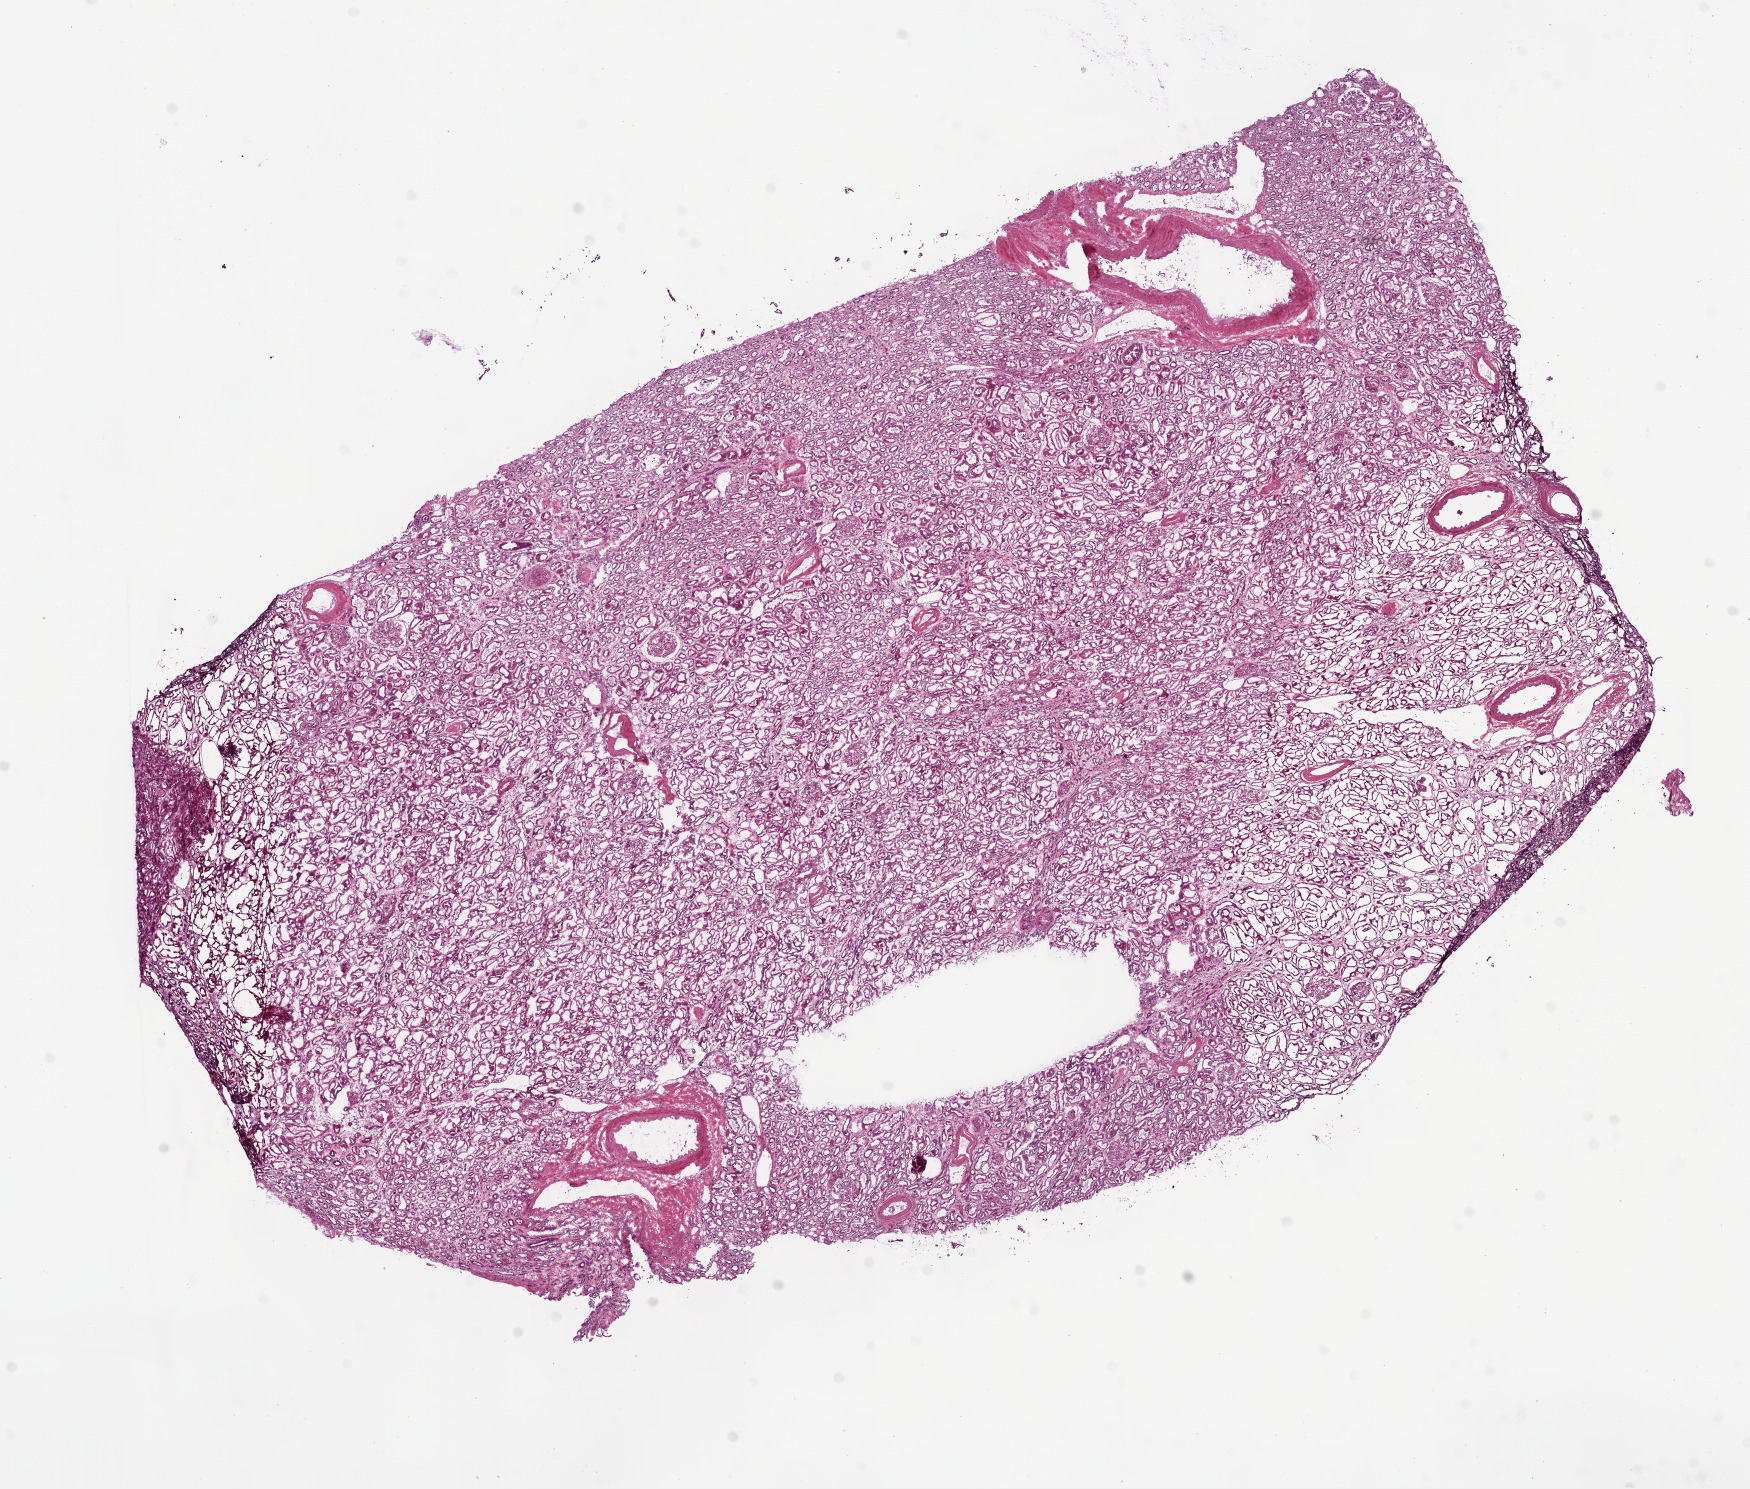
H&E whole-slide image — low-resolution overview of the scanned area, about 14.0 x 11.9 mm, frozen section, kidney, solid tissue normal (non-tumour tissue) sample. Male patient; age at initial diagnosis 63 years.
- this section: solid tissue normal sample (biorepository sample class)
- patient diagnosis: Clear cell adenocarcinoma, NOS